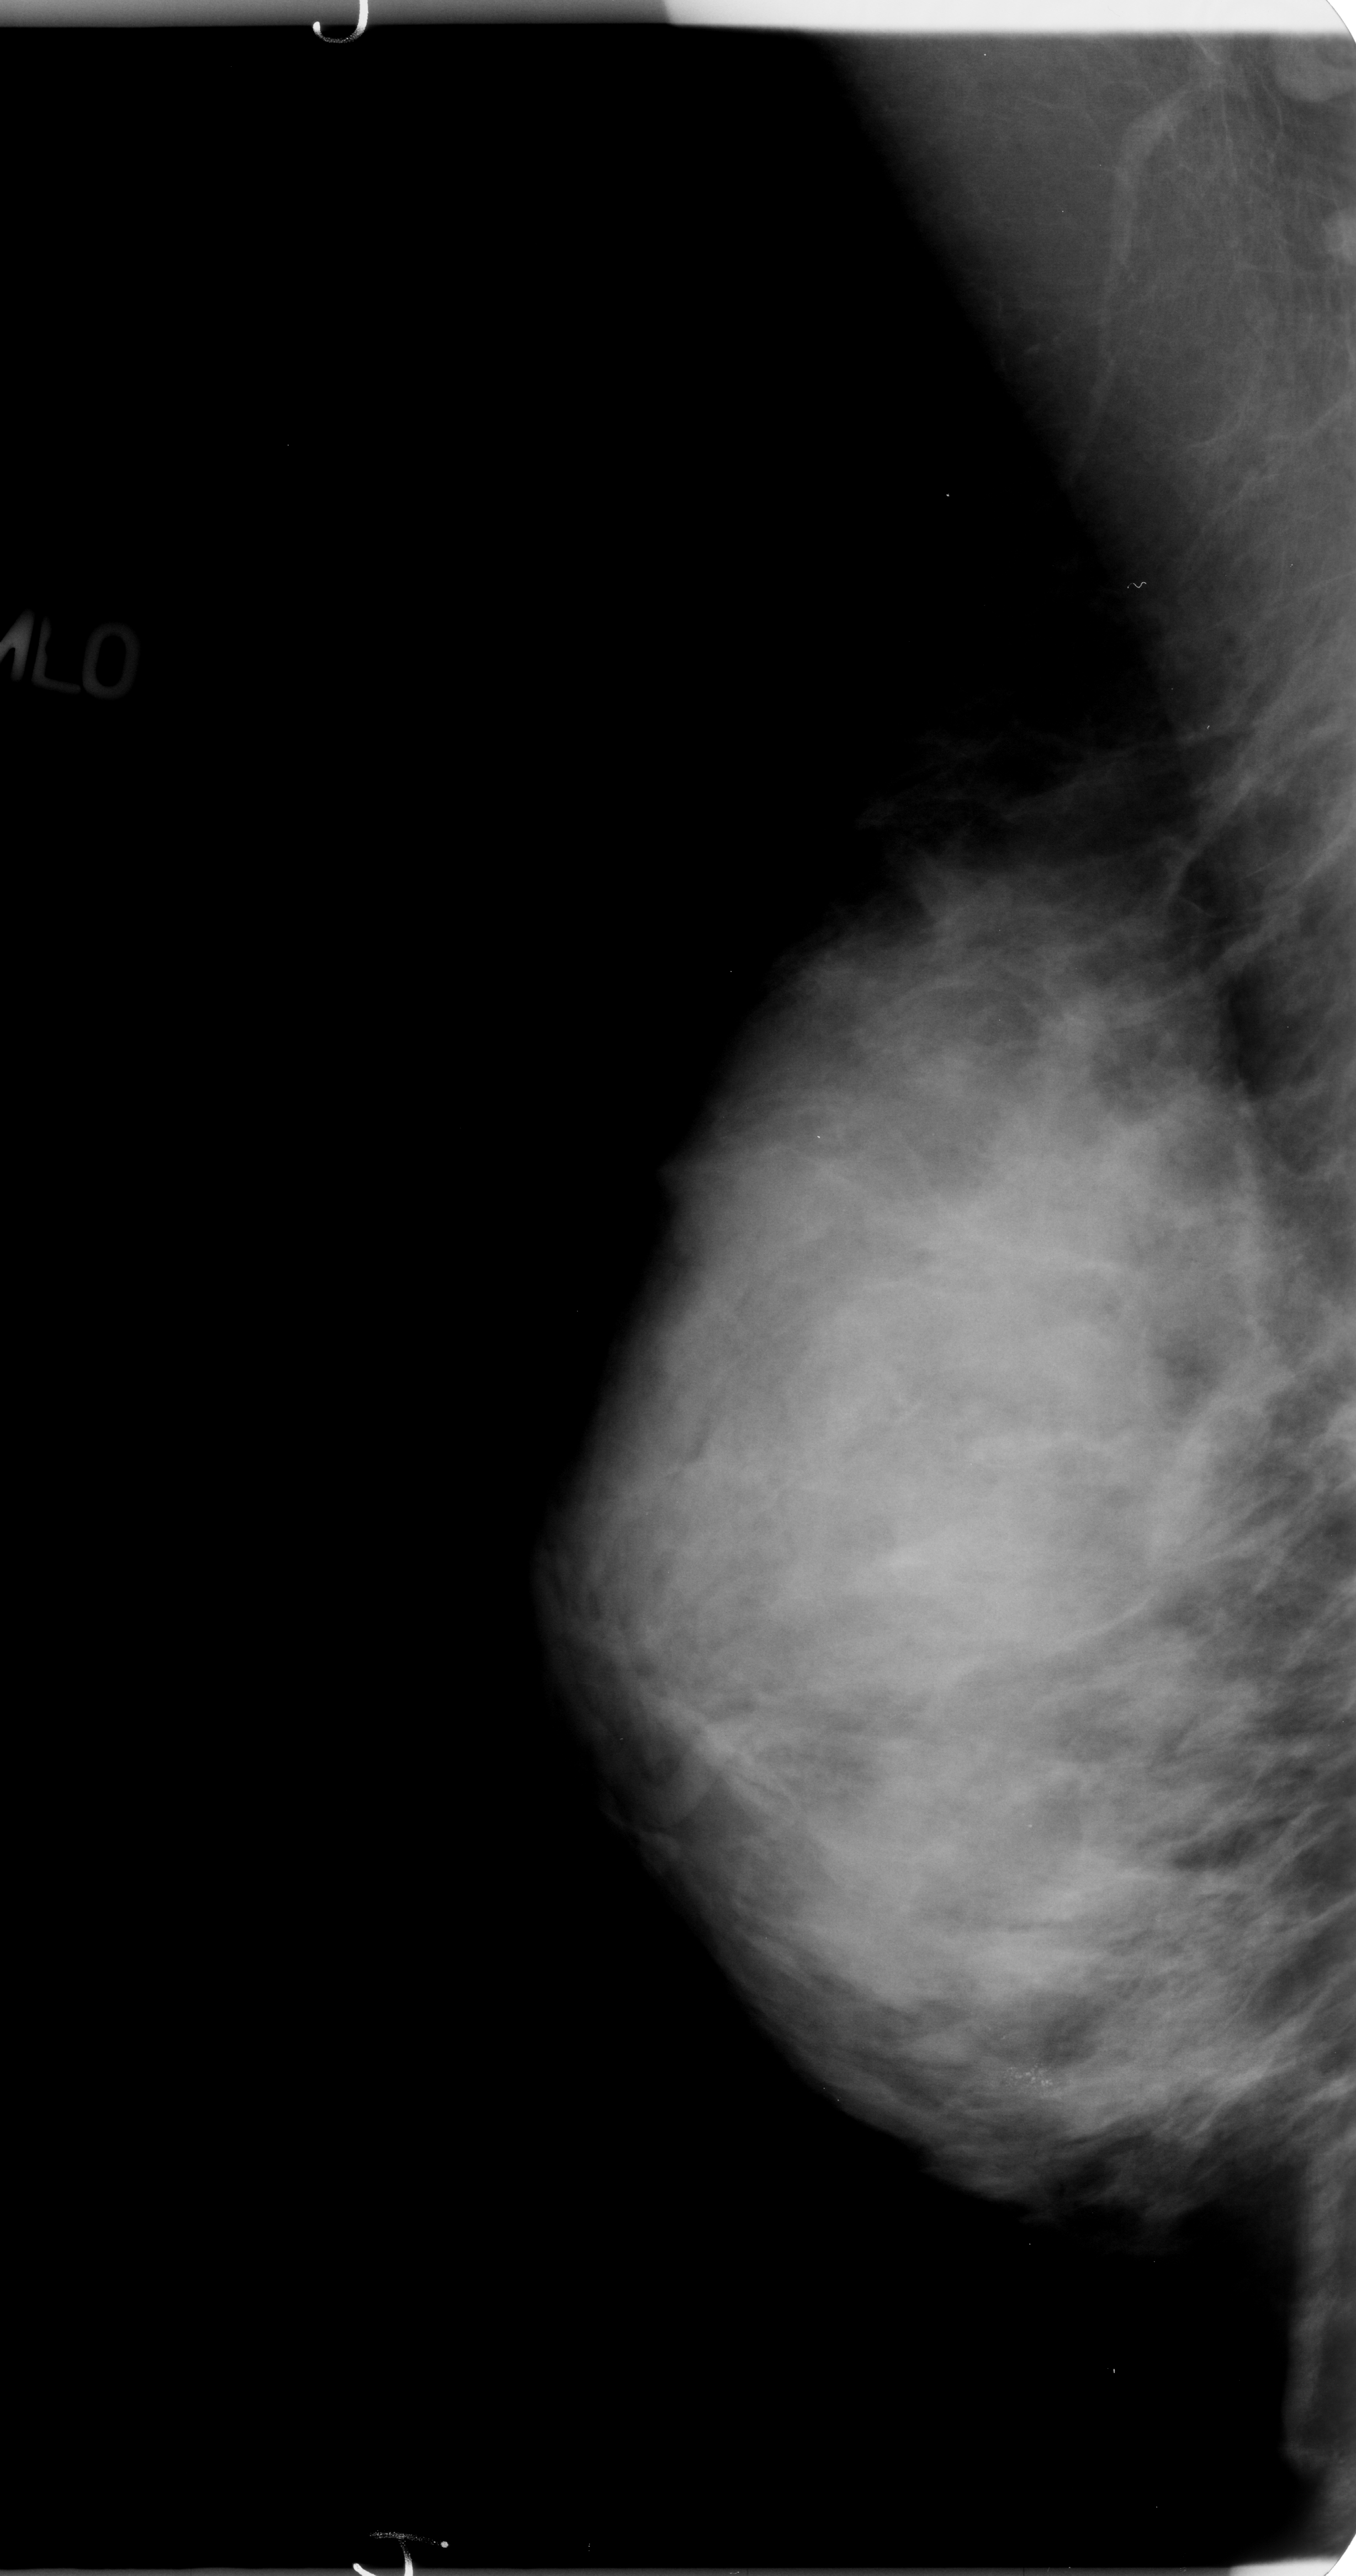
Digitized screen-film mammogram, right breast, mediolateral oblique (MLO) view, breast composition: extremely dense (BI-RADS density category 4 of 4).
Finding: calcifications, morphology pleomorphic, distribution clustered; BI-RADS assessment category 4; pathology result (as recorded, not read from the image): benign.